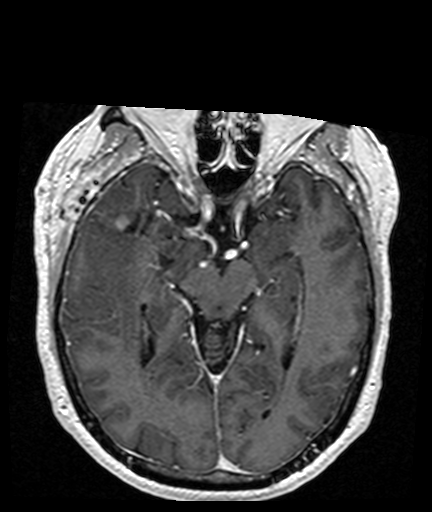
Brain MRI from a brain-tumour surgery series, one axial slice; position 101 of 176 along the scan axis; T1-weighted post-contrast; 432 × 512 image matrix, field of view 194 × 230 mm. From the clinical record (not read from this slice): histopathology: Glioblastoma; WHO grade: 4; IDH mutation: no.
Outlined on this slice (expert manual segmentation):
- tumour: bounding box <117,216,130,230> (left, top, right, bottom; pixels)